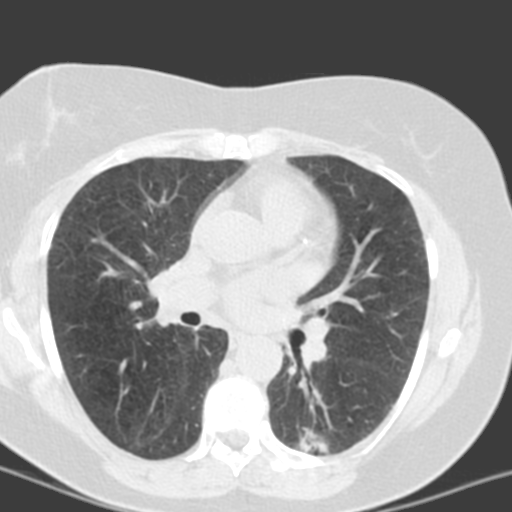
Chest CT (low-dose screening protocol), one axial image; third screening round (two years after baseline); lung window (W 1500 / L -600 HU); 3.2 mm slice thickness; standard (soft-tissue) reconstruction kernel (B); 512 × 512 image matrix, field of view 290 × 290 mm. Female participant, aged 55 years at enrolment. Current smoker at enrolment.
- Expert reader's lesion annotation, bounding box <285,410,364,463> (left, top, right, bottom; pixels).
- The screening reader recorded 6 non-calcified nodules or masses ≥4 mm on this exam (left lower lobe, left lower lobe, left upper lobe, lingula, lingula, right middle lobe); which of them this box marks is not recorded.
- Official screen result: positive, no significant change: stable abnormalities potentially related to lung cancer, unchanged since the prior screening exam.
- Lung cancer was diagnosed 357 days after this screen: adenocarcinoma with mixed subtypes, left lower lobe, poorly differentiated (G3), stage IA (AJCC 6th edition), 21 mm at pathology.